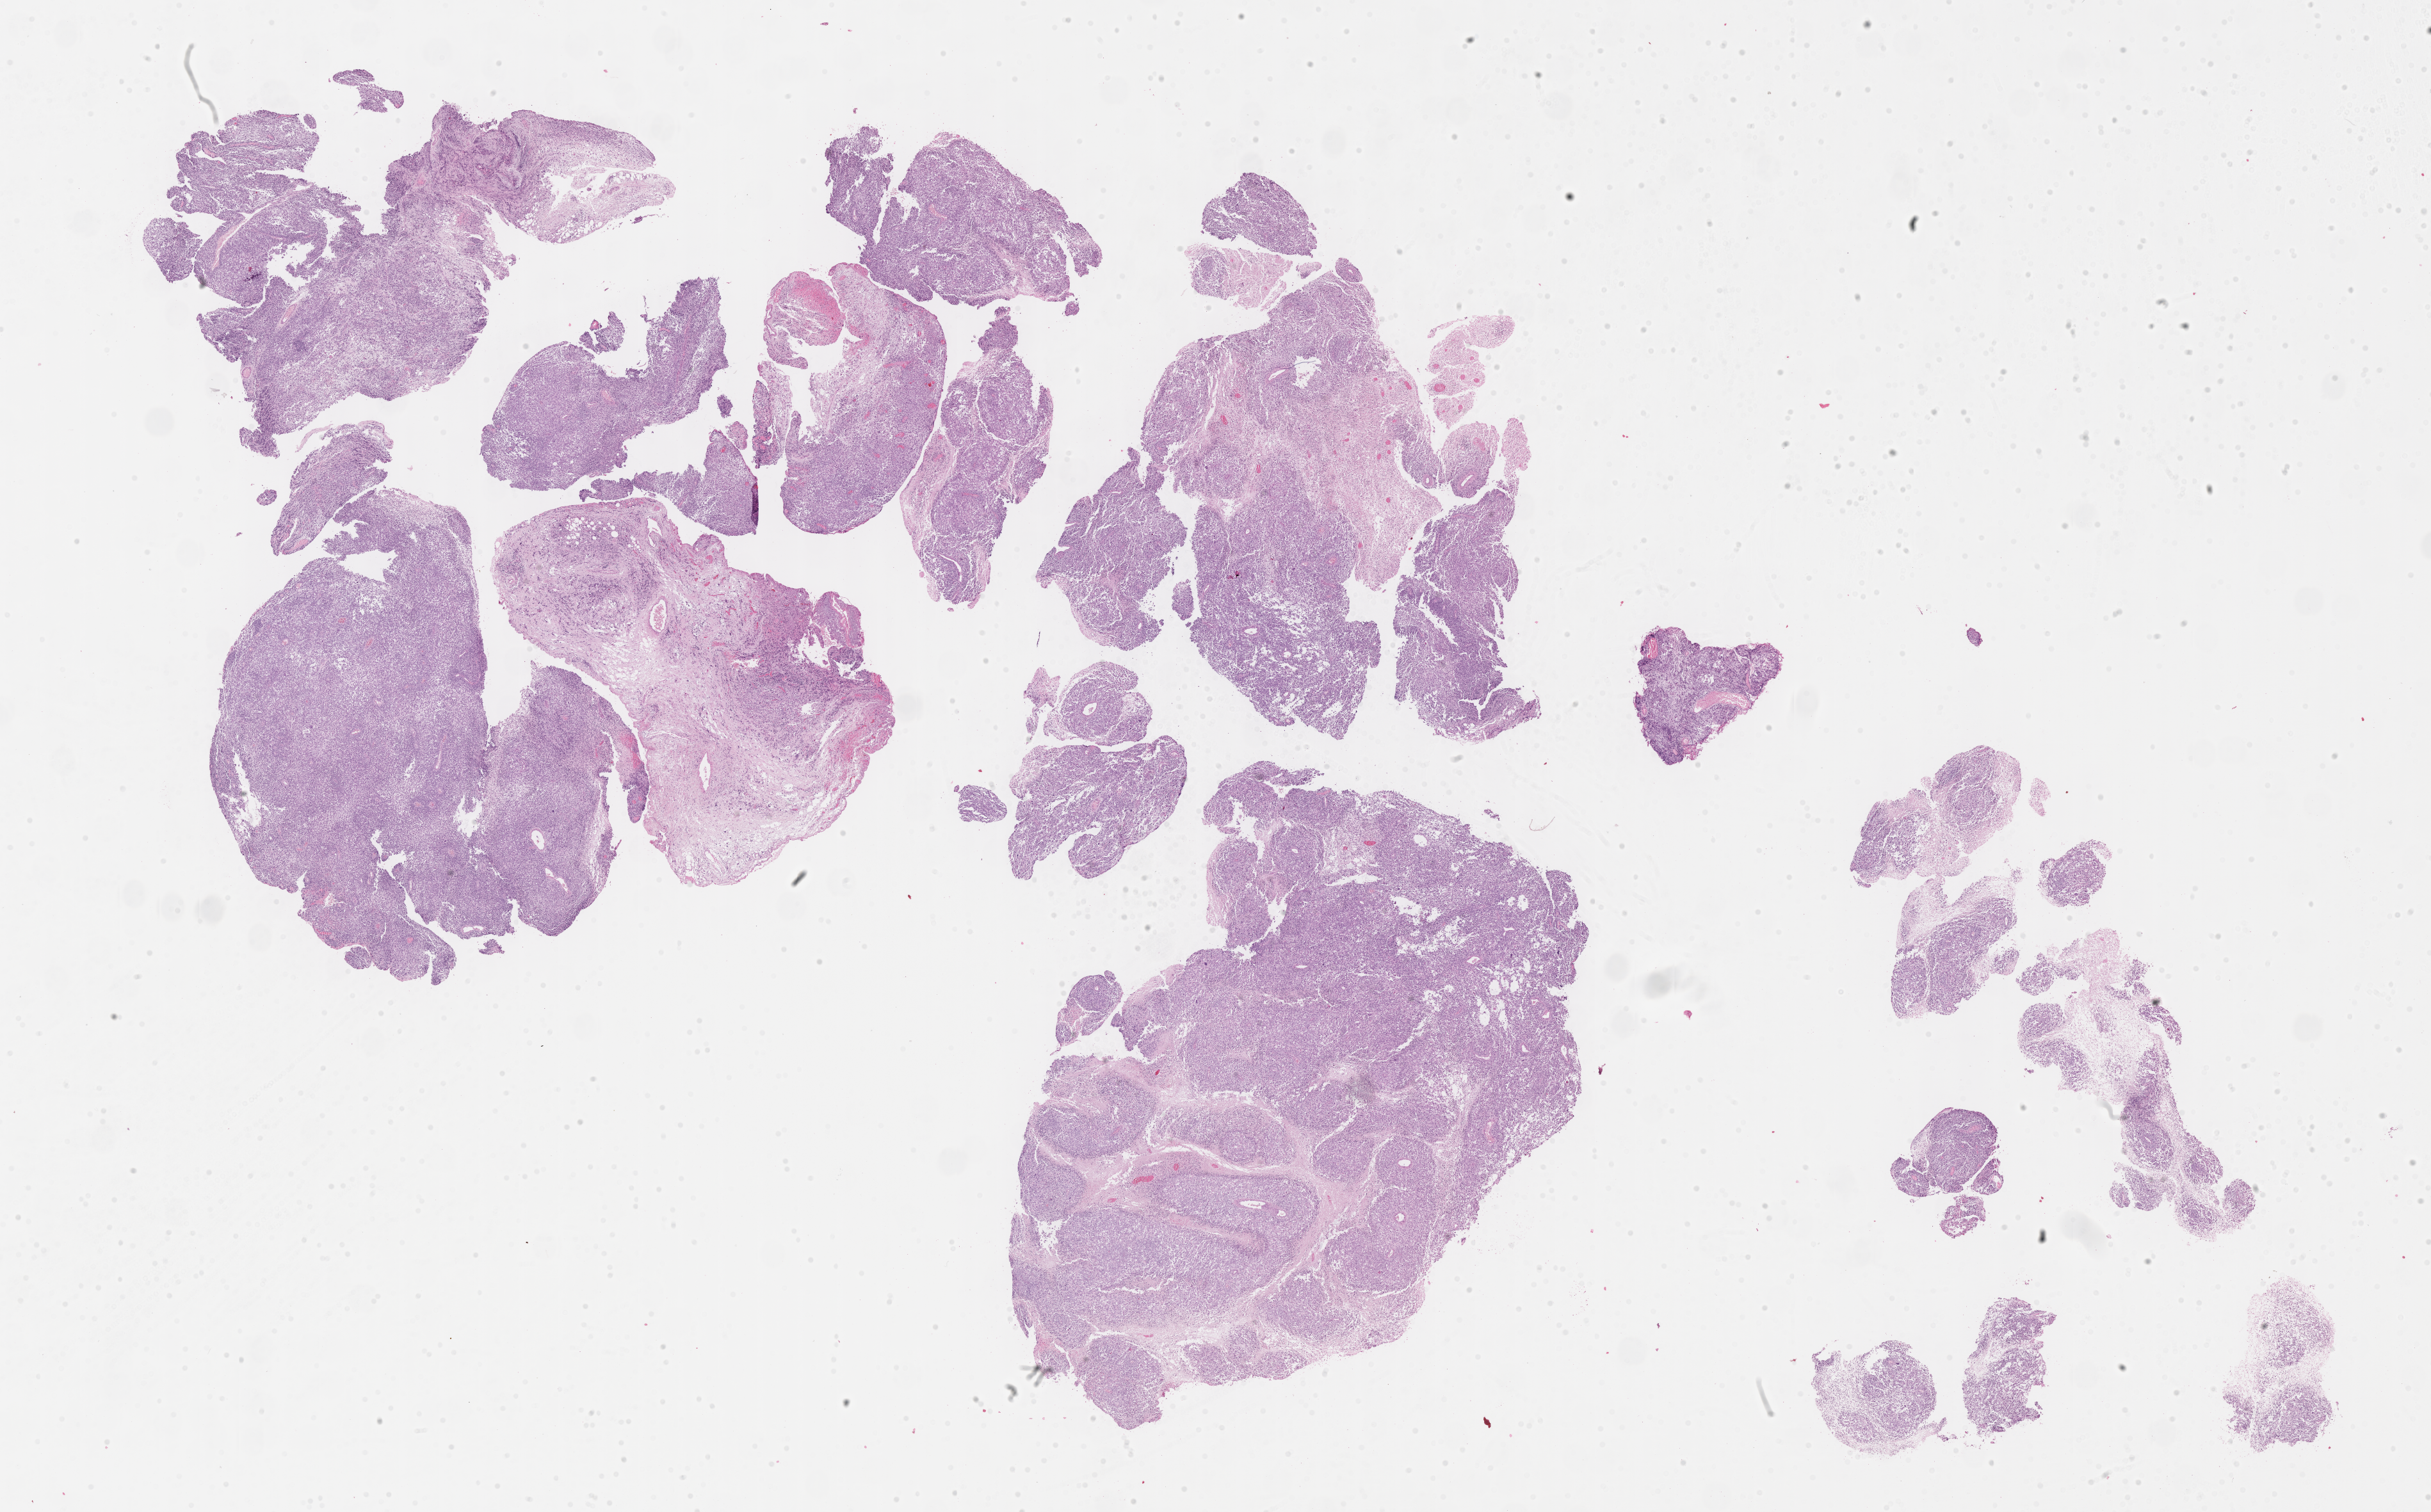
Haematoxylin and eosin whole-slide image of tumor tissue, shown as a low-resolution overview of the whole scanned area (about 30.7 x 19.1 mm), FFPE section, site: orbit, right. Female patient, age at diagnosis 6.7 years.
Metastatic status at presentation (as recorded): non-metastatic. Stage (as recorded): 1. Diagnosis: rhabdomyosarcoma; histological classification: embryonal rhabdomyosarcoma.